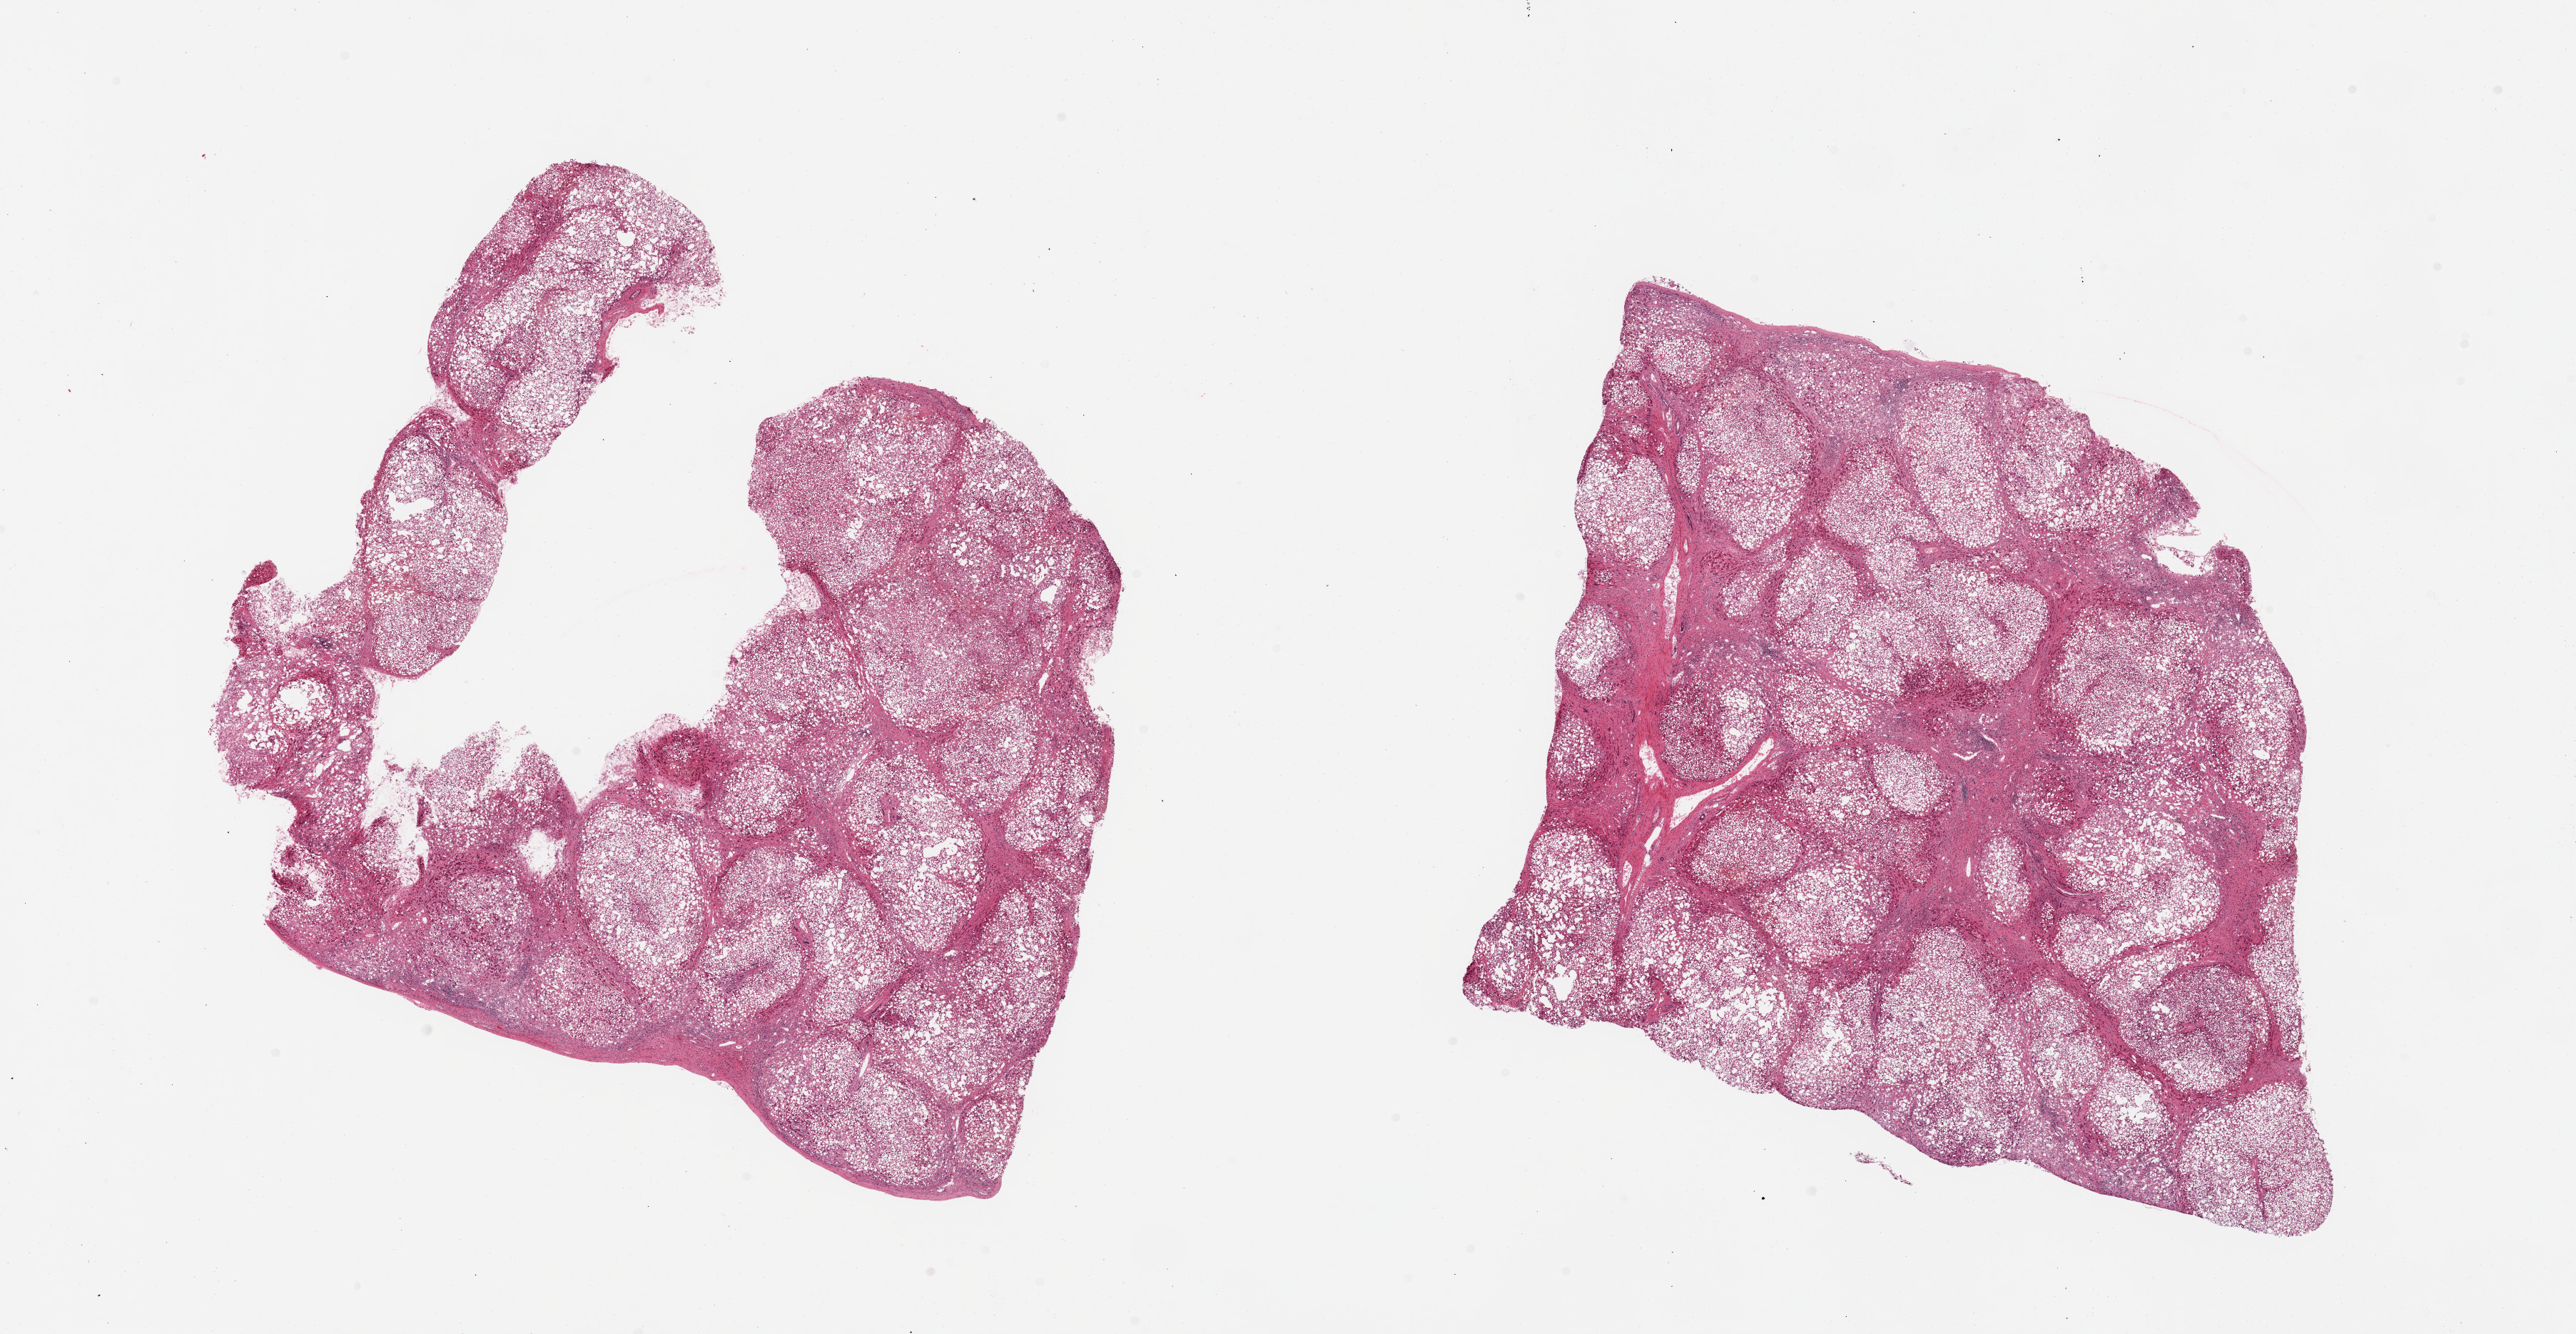
H&E whole-slide image, a low-resolution overview of the entire scanned area, about 28.5 x 14.8 mm. PAXgene-fixed, paraffin-embedded tissue. Target tissue: liver. Donor tissue sample. Donor: male.
Reviewer comment on this tissue sample: 2 pieces; includes capsule (target is 1cm below capsule), cirrhosis with severe microvesicular and macrovesicuar steatosis, Mallory hylaine.